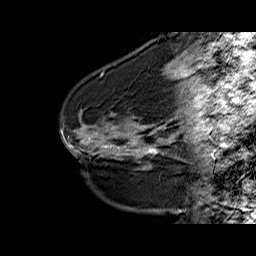
Breast MRI (dynamic contrast-enhanced), one sagittal slice; position 17 of 60 along the scan axis; dynamic contrast-enhanced series, time point 2 of 6 at this slice position (early post-contrast); 1.5 T; TE 6.3 ms, TR 32.5 ms; 4 mm slice thickness; 256 × 256 image matrix, field of view 200 × 200 mm. Female patient. Case-level facts recorded for this patient, not image findings: setting: breast cancer imaged before/during neoadjuvant chemotherapy; receptor status: HR-positive, HER2-negative.
Outlined on this slice (semi-automatically segmented with operator editing):
- analysis volume of interest (the breast-tissue region the enhancement analysis was run in; not a lesion): box from (x=94, y=112) to (x=161, y=163) px
- tumour enhancement mask (voxels above the 100 % enhancement threshold inside the analysis volume of interest): (x=146, y=148)–(x=157, y=153)